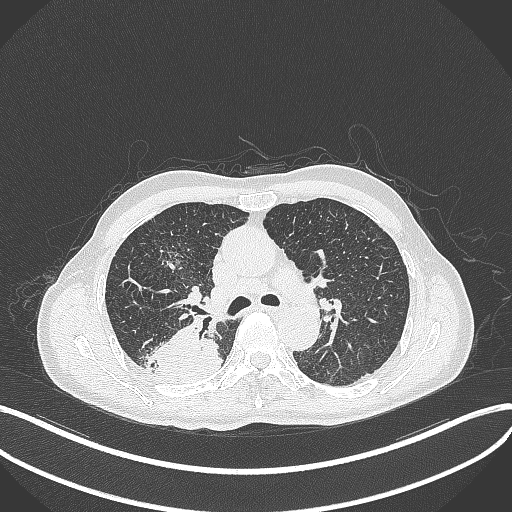
Chest CT, one axial slice. Reconstruction kernel B70f. 120 kVp. Lung window (W 1500 / L -600 HU). 1 mm slice thickness. 512 × 512 image matrix, field of view 400 × 400 mm. Male patient, age 79 years. From the clinical record (not read from this slice): clinical TNM (as recorded): T3 N0 M0.
Structures marked on this image (rectangle marked by the reading radiologist):
- lung tumour (recorded histology: adenocarcinoma): box from (x=150, y=318) to (x=220, y=379) px